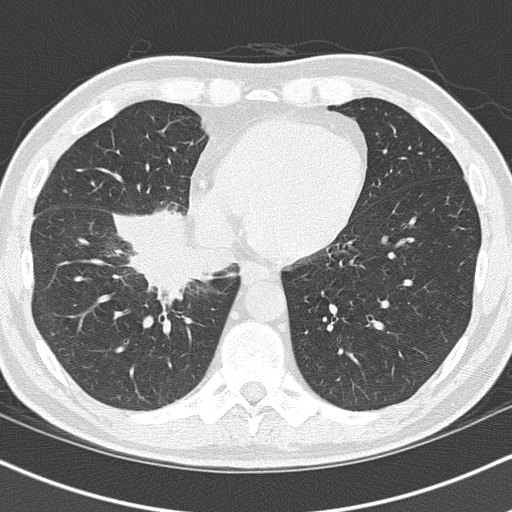
Chest CT (low-dose screening protocol), one axial image. Baseline annual screen. Lung window (W 1500 / L -600 HU). 2 mm slice thickness. 512 × 512 image matrix. Male, age 55 years at enrolment. Current smoker at enrolment.
• Lesion marked by an expert reader, box from (x=121, y=222) to (x=243, y=315) px.
• Screening reader's record for this exam (one nodule recorded; not confirmed to be the boxed lesion): non-calcified nodule or mass ≥4 mm, right lower lobe, 6 × 5 mm, spiculated (stellate) margins, soft tissue attenuation.
• Official screen result: positive, change unspecified: nodule(s) >= 4 mm or enlarging nodule(s), mass(es), or other non-specific abnormalities suspicious for lung cancer.
• Later outcome: lung cancer diagnosed 21 days after this screen — carcinoma, NOS, right hilum, stage IB (AJCC 6th edition), 67 mm at pathology.